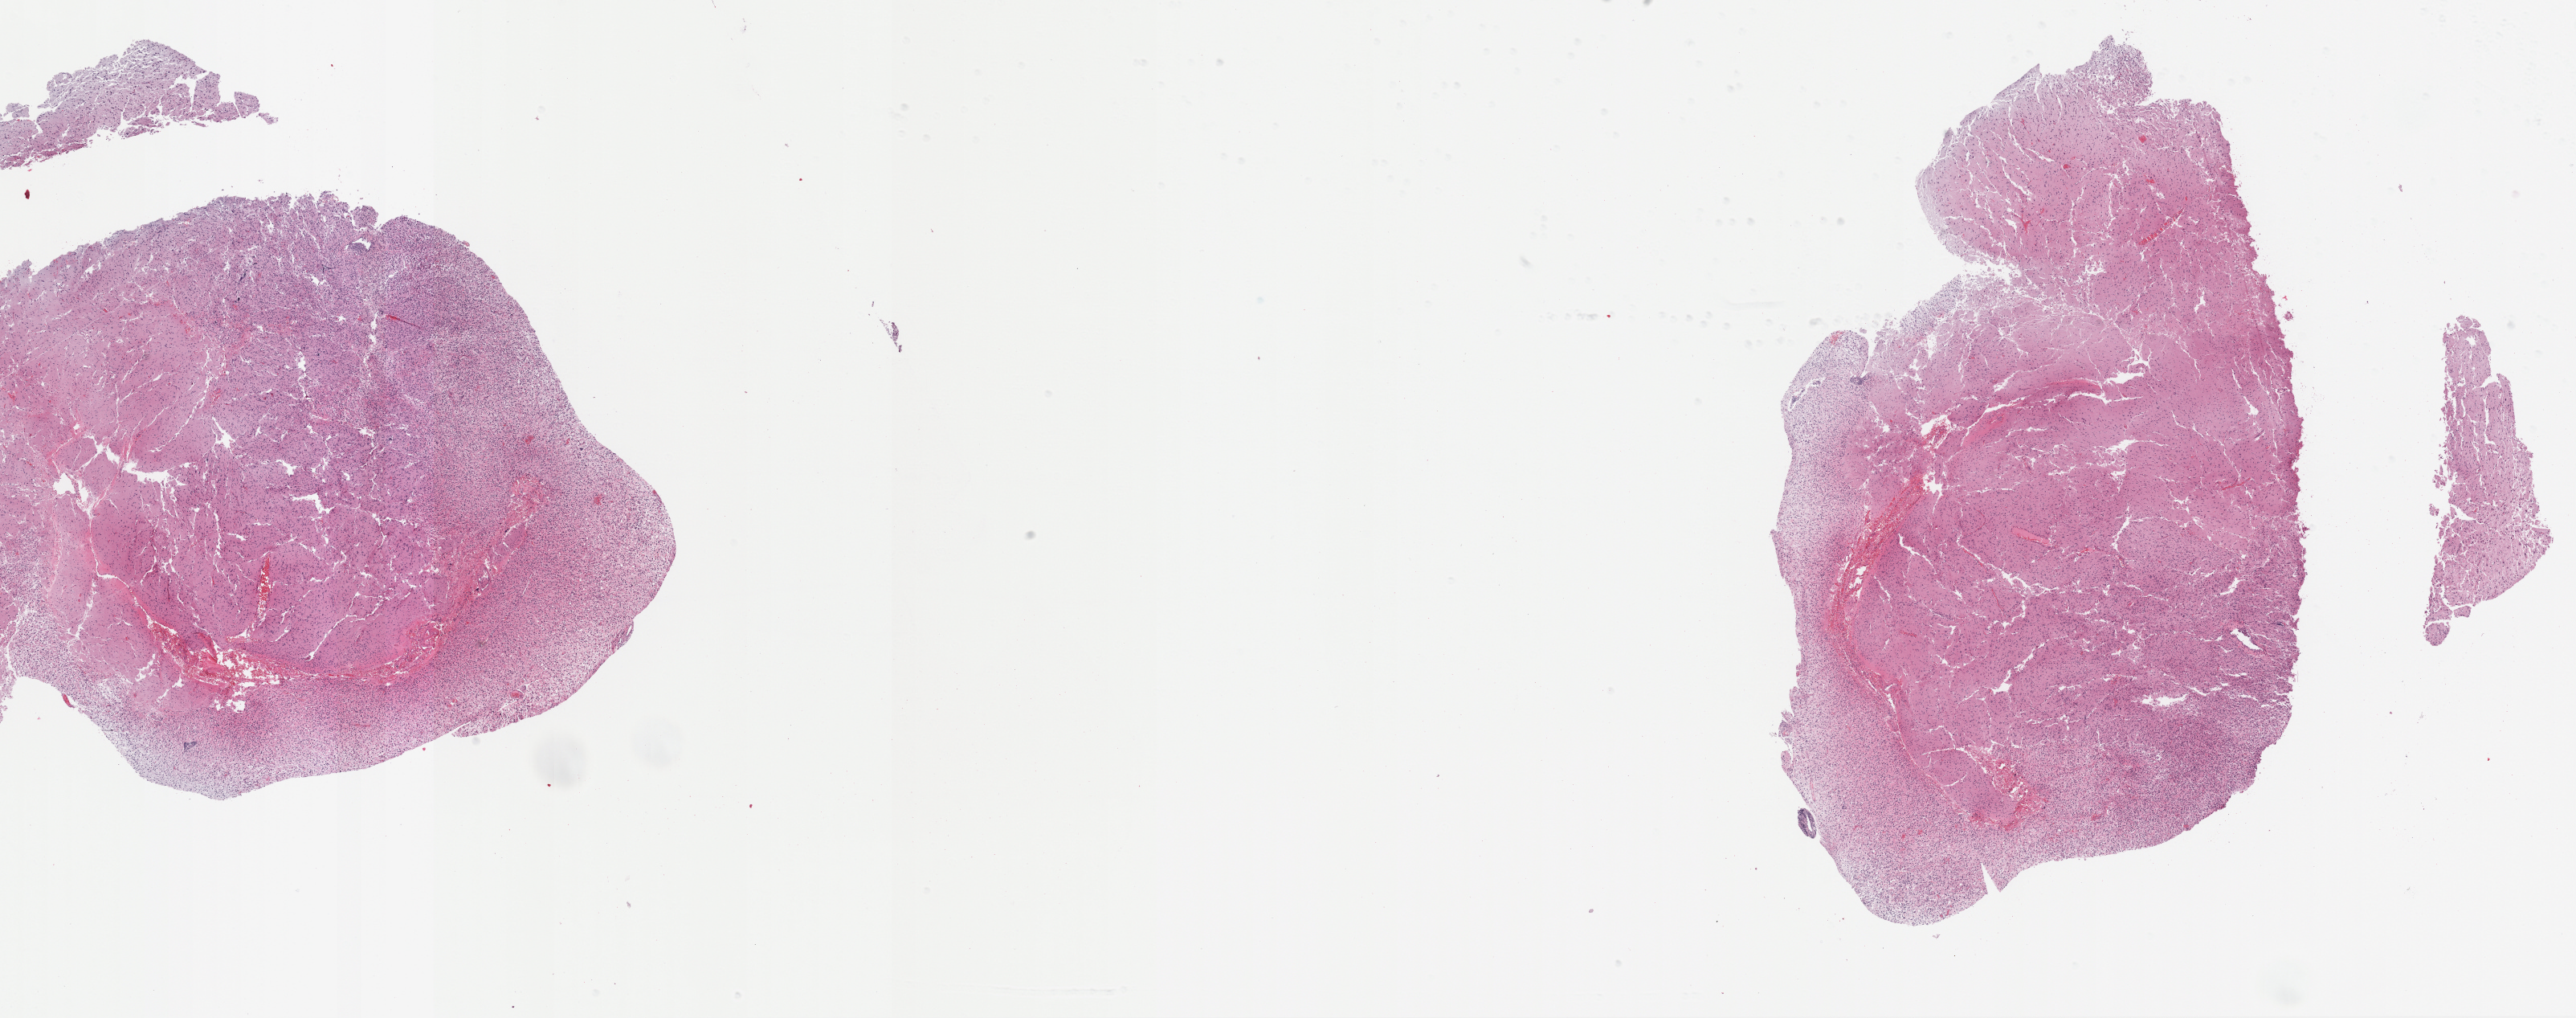
H&E whole-slide image, whole scanned area (about 25.9 x 10.2 mm, from a 40x scan) shown as a low-resolution overview, formalin-fixed paraffin-embedded (FFPE) diagnostic section, brain, primary tumour sample. Male patient; age at initial diagnosis 23 years. Histologic grade: G3 (poorly differentiated).
Pathologic diagnosis: Mixed glioma (cerebrum). Laterality: left.